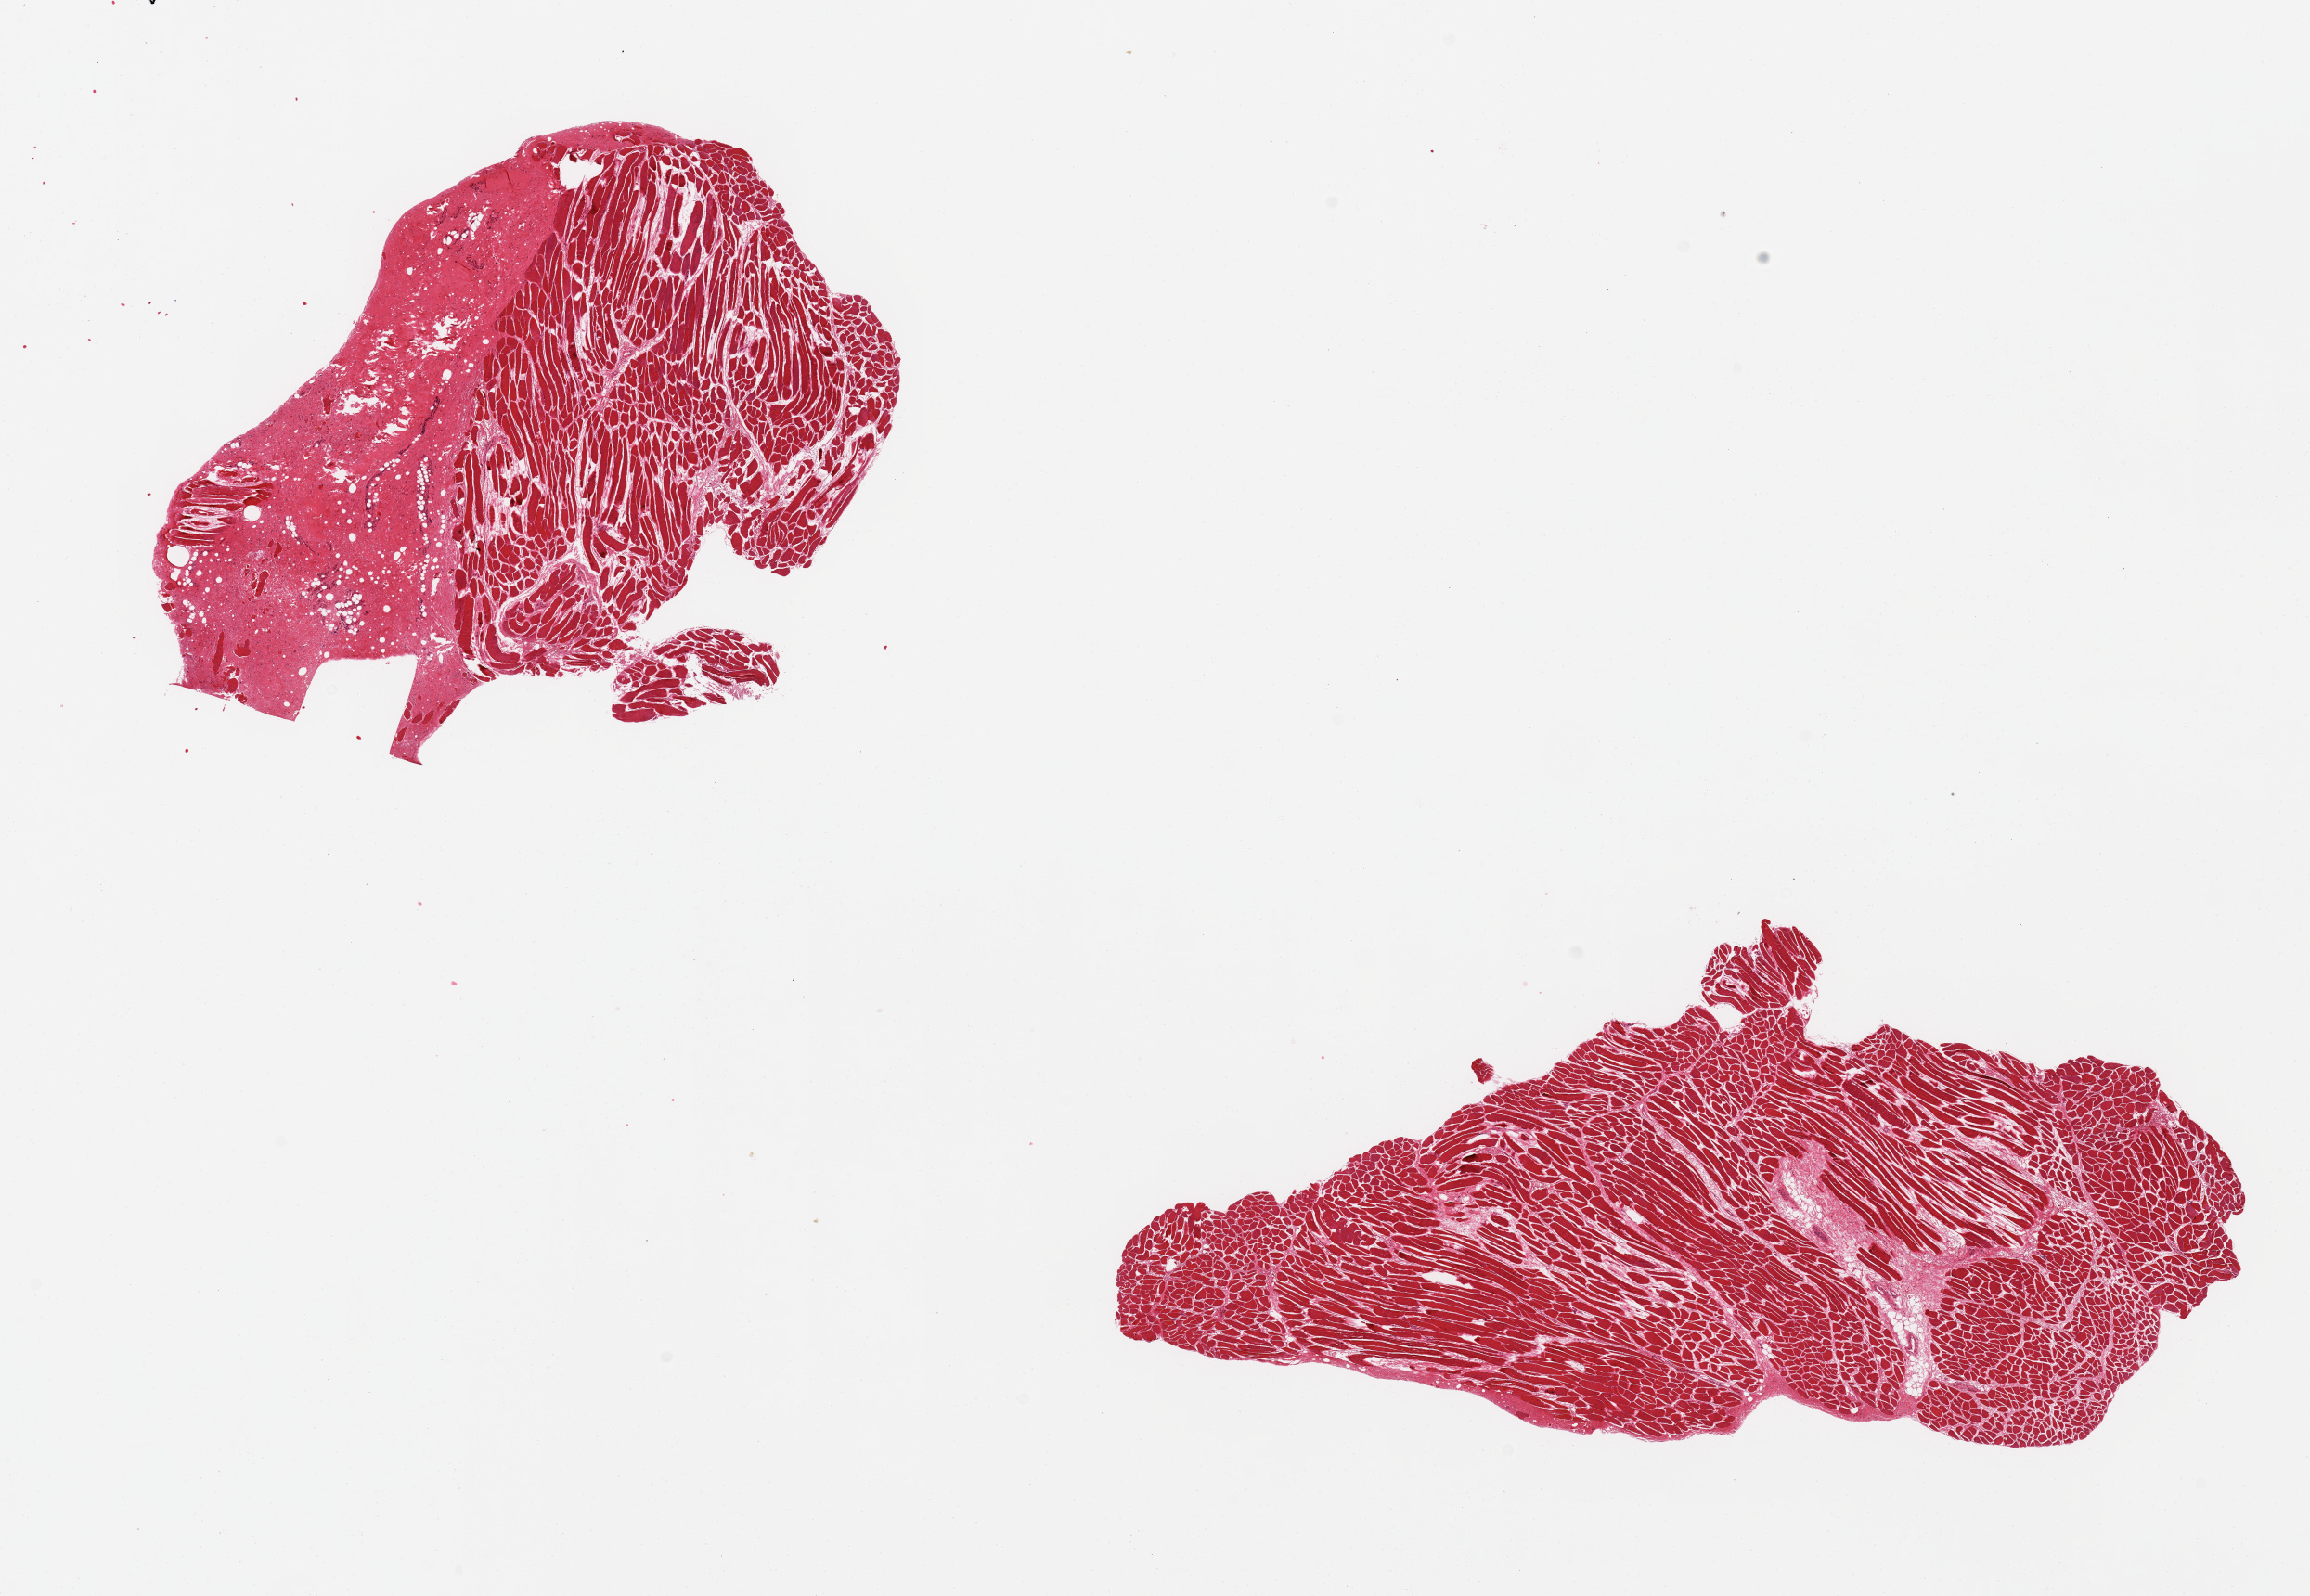
Whole-slide image, H&E stain, brightfield, a low-resolution overview of the entire scanned area, about 19.7 x 13.6 mm; PAXgene-fixed, paraffin-embedded tissue; sampled site (target tissue): thyroid; donor tissue sample.
Reviewer comment on this tissue sample: 2 pieces; no thyroid, only skeletal muscle.